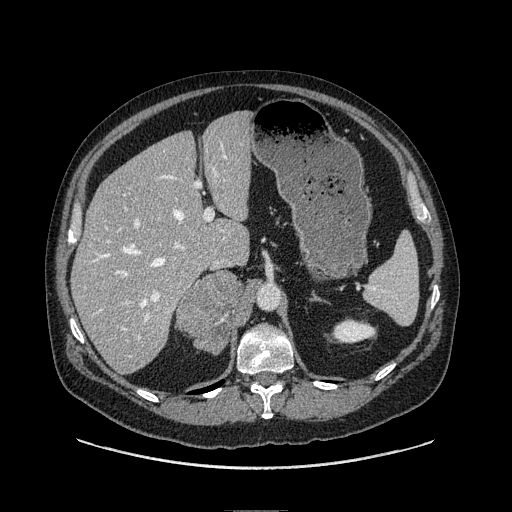
Contrast-enhanced abdominal CT, one axial slice. Position 62 of 149 along the scan axis. Soft-tissue window (W 400 / L 40 HU). 512 × 512 image matrix, field of view 440 × 440 mm. Male patient. From the clinical record (not read from this slice): diagnosis: adrenocortical carcinoma; tumour side: right adrenal; tumour size at pathology: 7.5 cm; Ki-67 index: 15 %; stage (as recorded): 2.
Annotated regions visible in this slice (semi-automatically segmented with operator editing):
- mass: box from (x=178, y=272) to (x=246, y=352) px